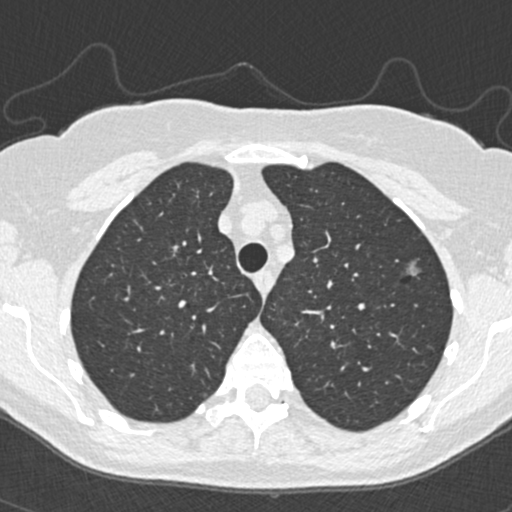
Low-dose screening chest CT, one axial slice. Slice 280 of 350 in the series (ordered by position). Reconstruction kernel B30f. 120 kVp. Lung window (W 1500 / L -600 HU). 1 mm slice thickness. 512 × 512 image matrix.
Structures marked on this image (expert manual segmentation):
- lesion 3 (tumor, upper lobe of left lung): box from (x=408, y=263) to (x=419, y=277) px